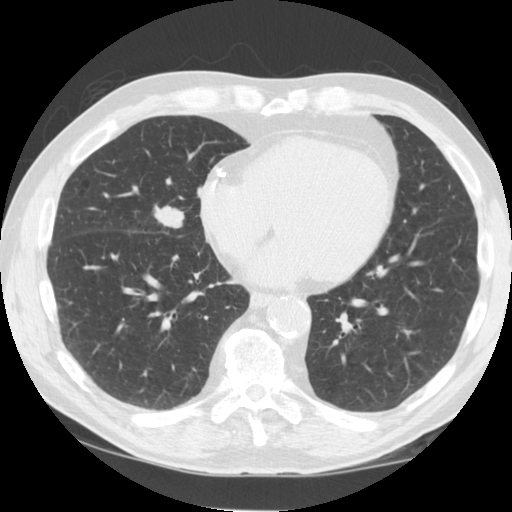
Axial slice from a low-dose chest CT screening exam. Third annual screen. Lung window (W 1500 / L -600 HU). 2.5 mm slice thickness. 120 kVp. Slice 84 of 125 in the series. Male participant, aged 64 years at enrolment. Current smoker at enrolment.
Lesion marked by an expert reader, bounding box [x1, y1, x2, y2] px = [133, 192, 202, 246]. The exam's reader record, not a measurement of the box and not confirmed to be the same lesion: non-calcified nodule or mass ≥4 mm, right middle lobe, 21 × 14 mm, smooth margins, soft tissue attenuation, pre-existing on the prior screen: yes; interval growth: yes.